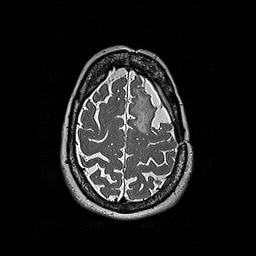
Brain MRI from a brain-tumour surgery series, one axial slice; 256 × 256 image matrix. Case-level facts recorded for this patient, not image findings: histopathology: Oligodendroglioma; WHO grade: 2; IDH mutation: yes; tumour location: Left Frontal.
Structures marked on this image (expert manual segmentation):
- tumour: box from (x=145, y=112) to (x=153, y=127) px